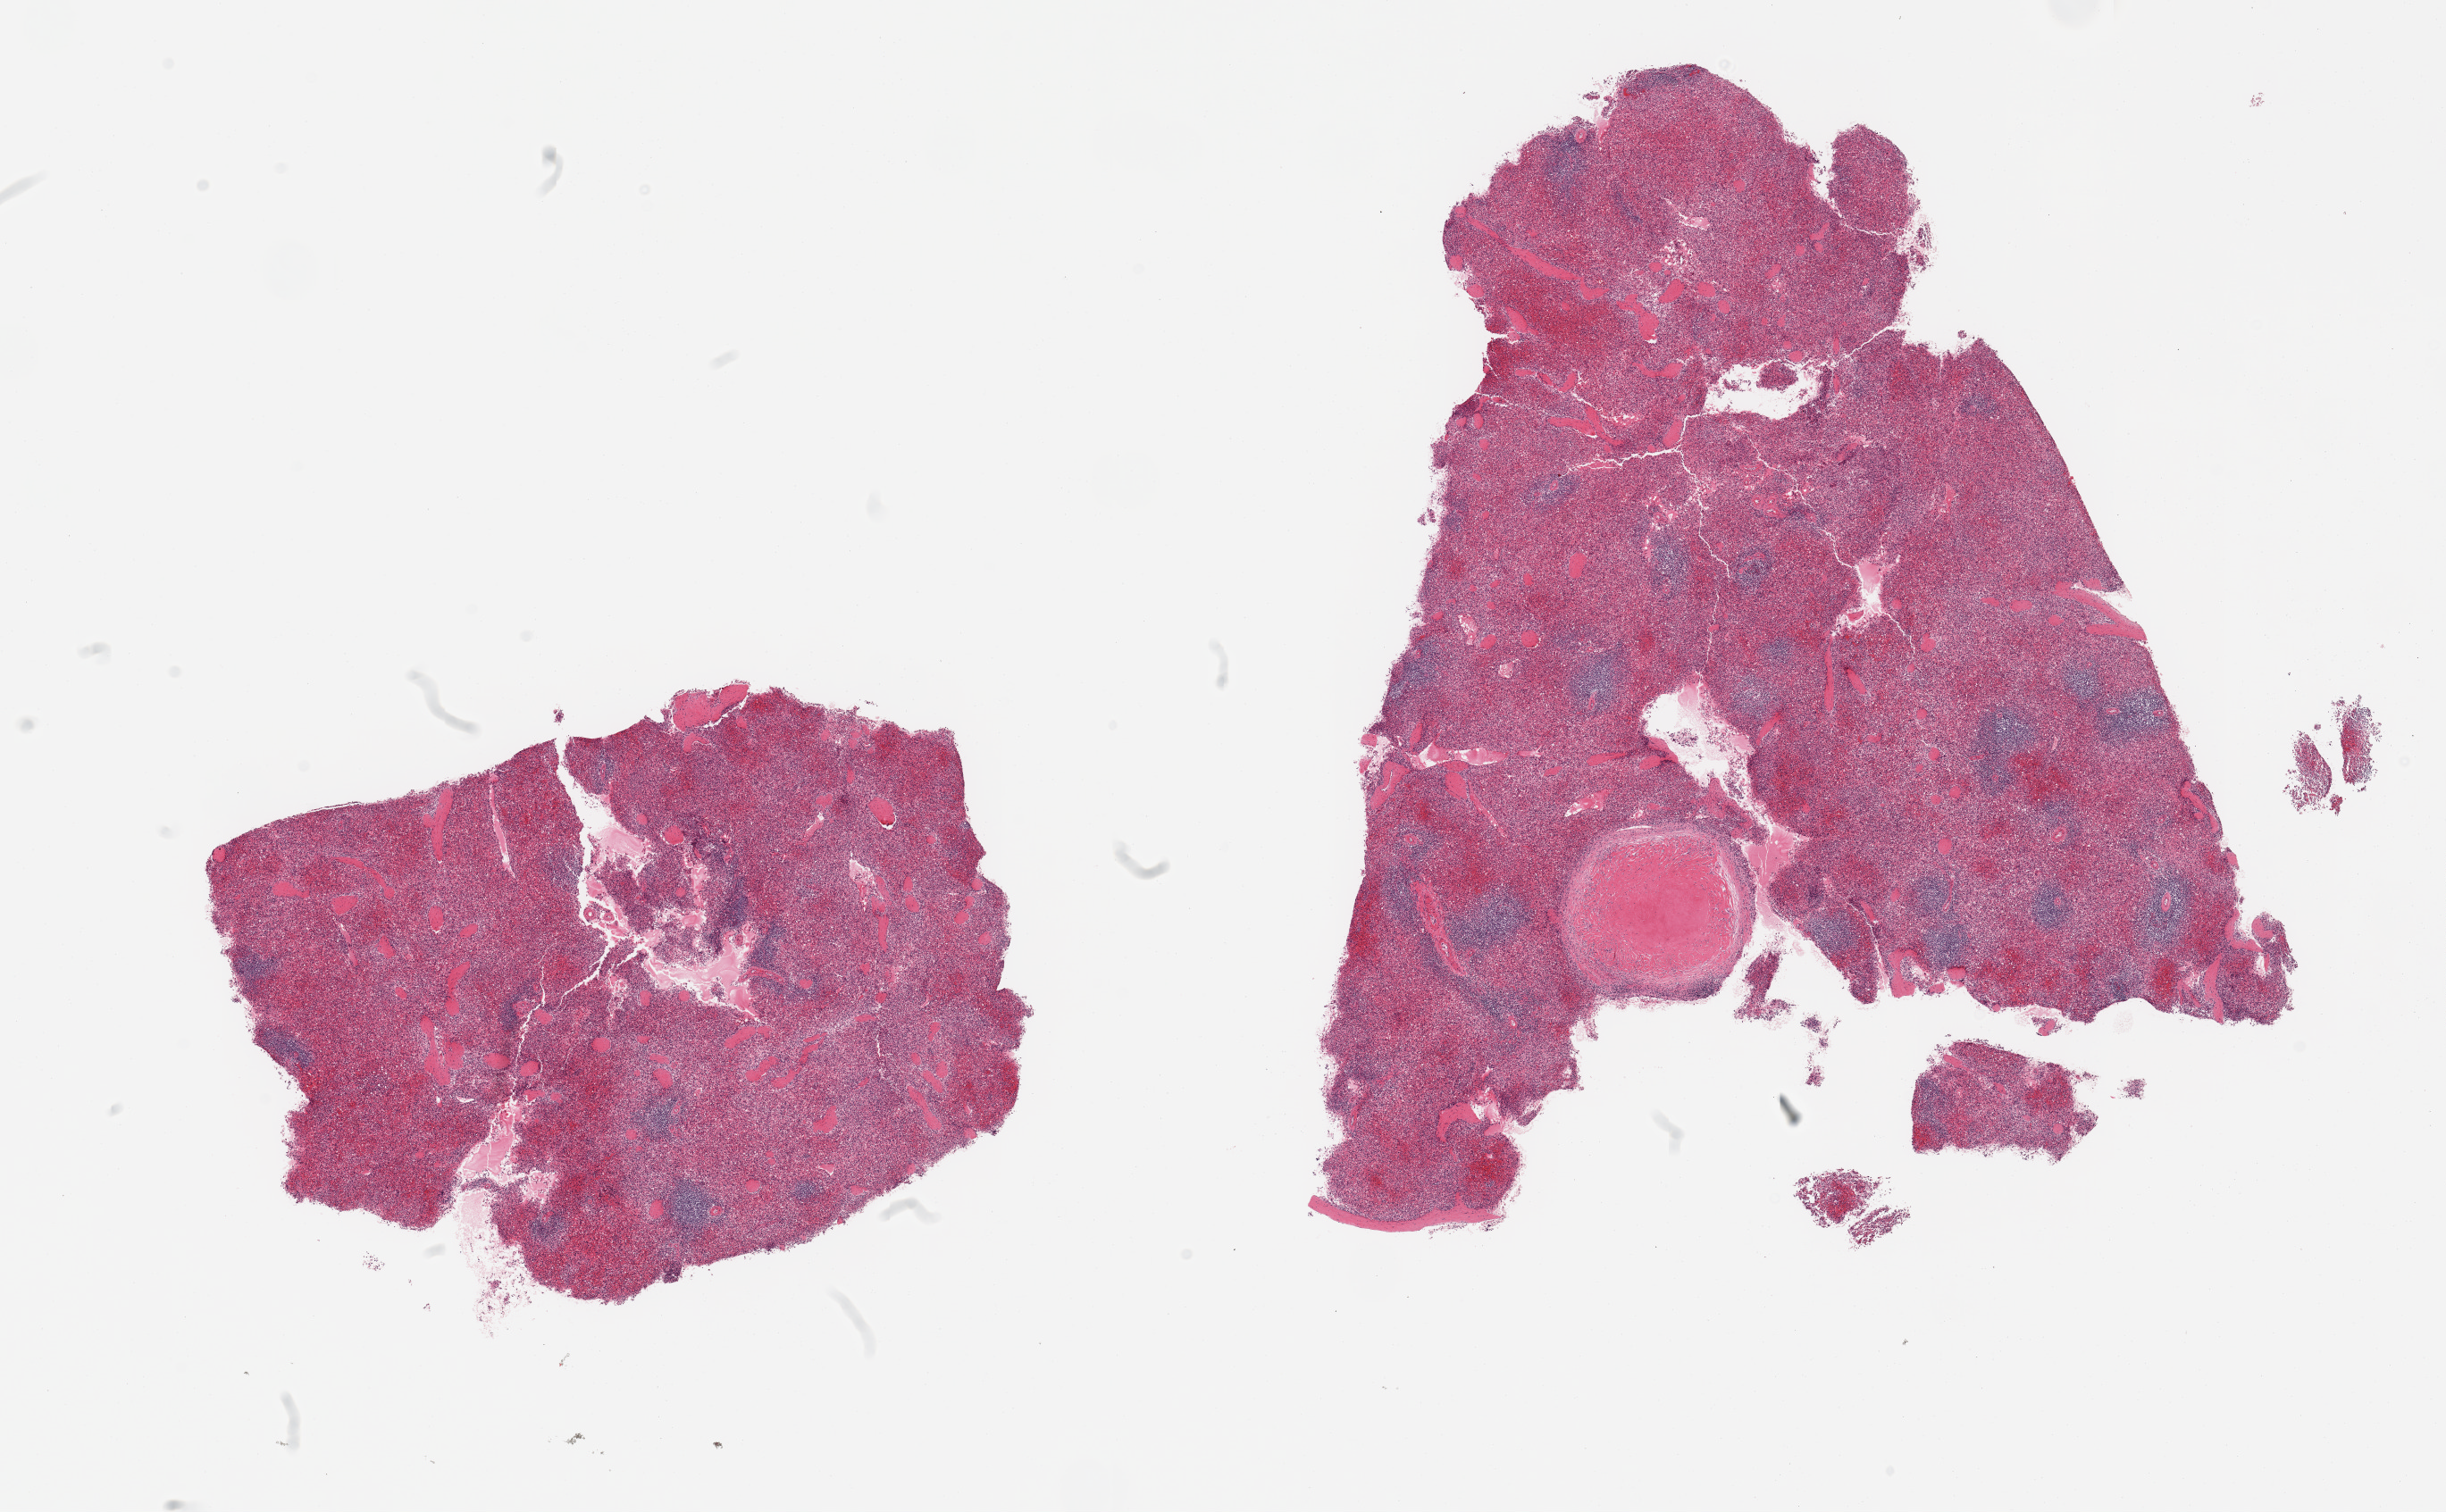
Digitized haematoxylin and eosin-stained section, whole scanned area (about 21.7 x 13.4 mm, from a 20x scan) shown as a low-resolution overview, PAXgene-fixed, paraffin-embedded tissue, target tissue: spleen, tissue donor sample.
• pathologist's review note for this sample: 2 pieces; includes portion of capsule (target is 5mm below capsule), 1.5mm fibrotic nodule/old granuloma